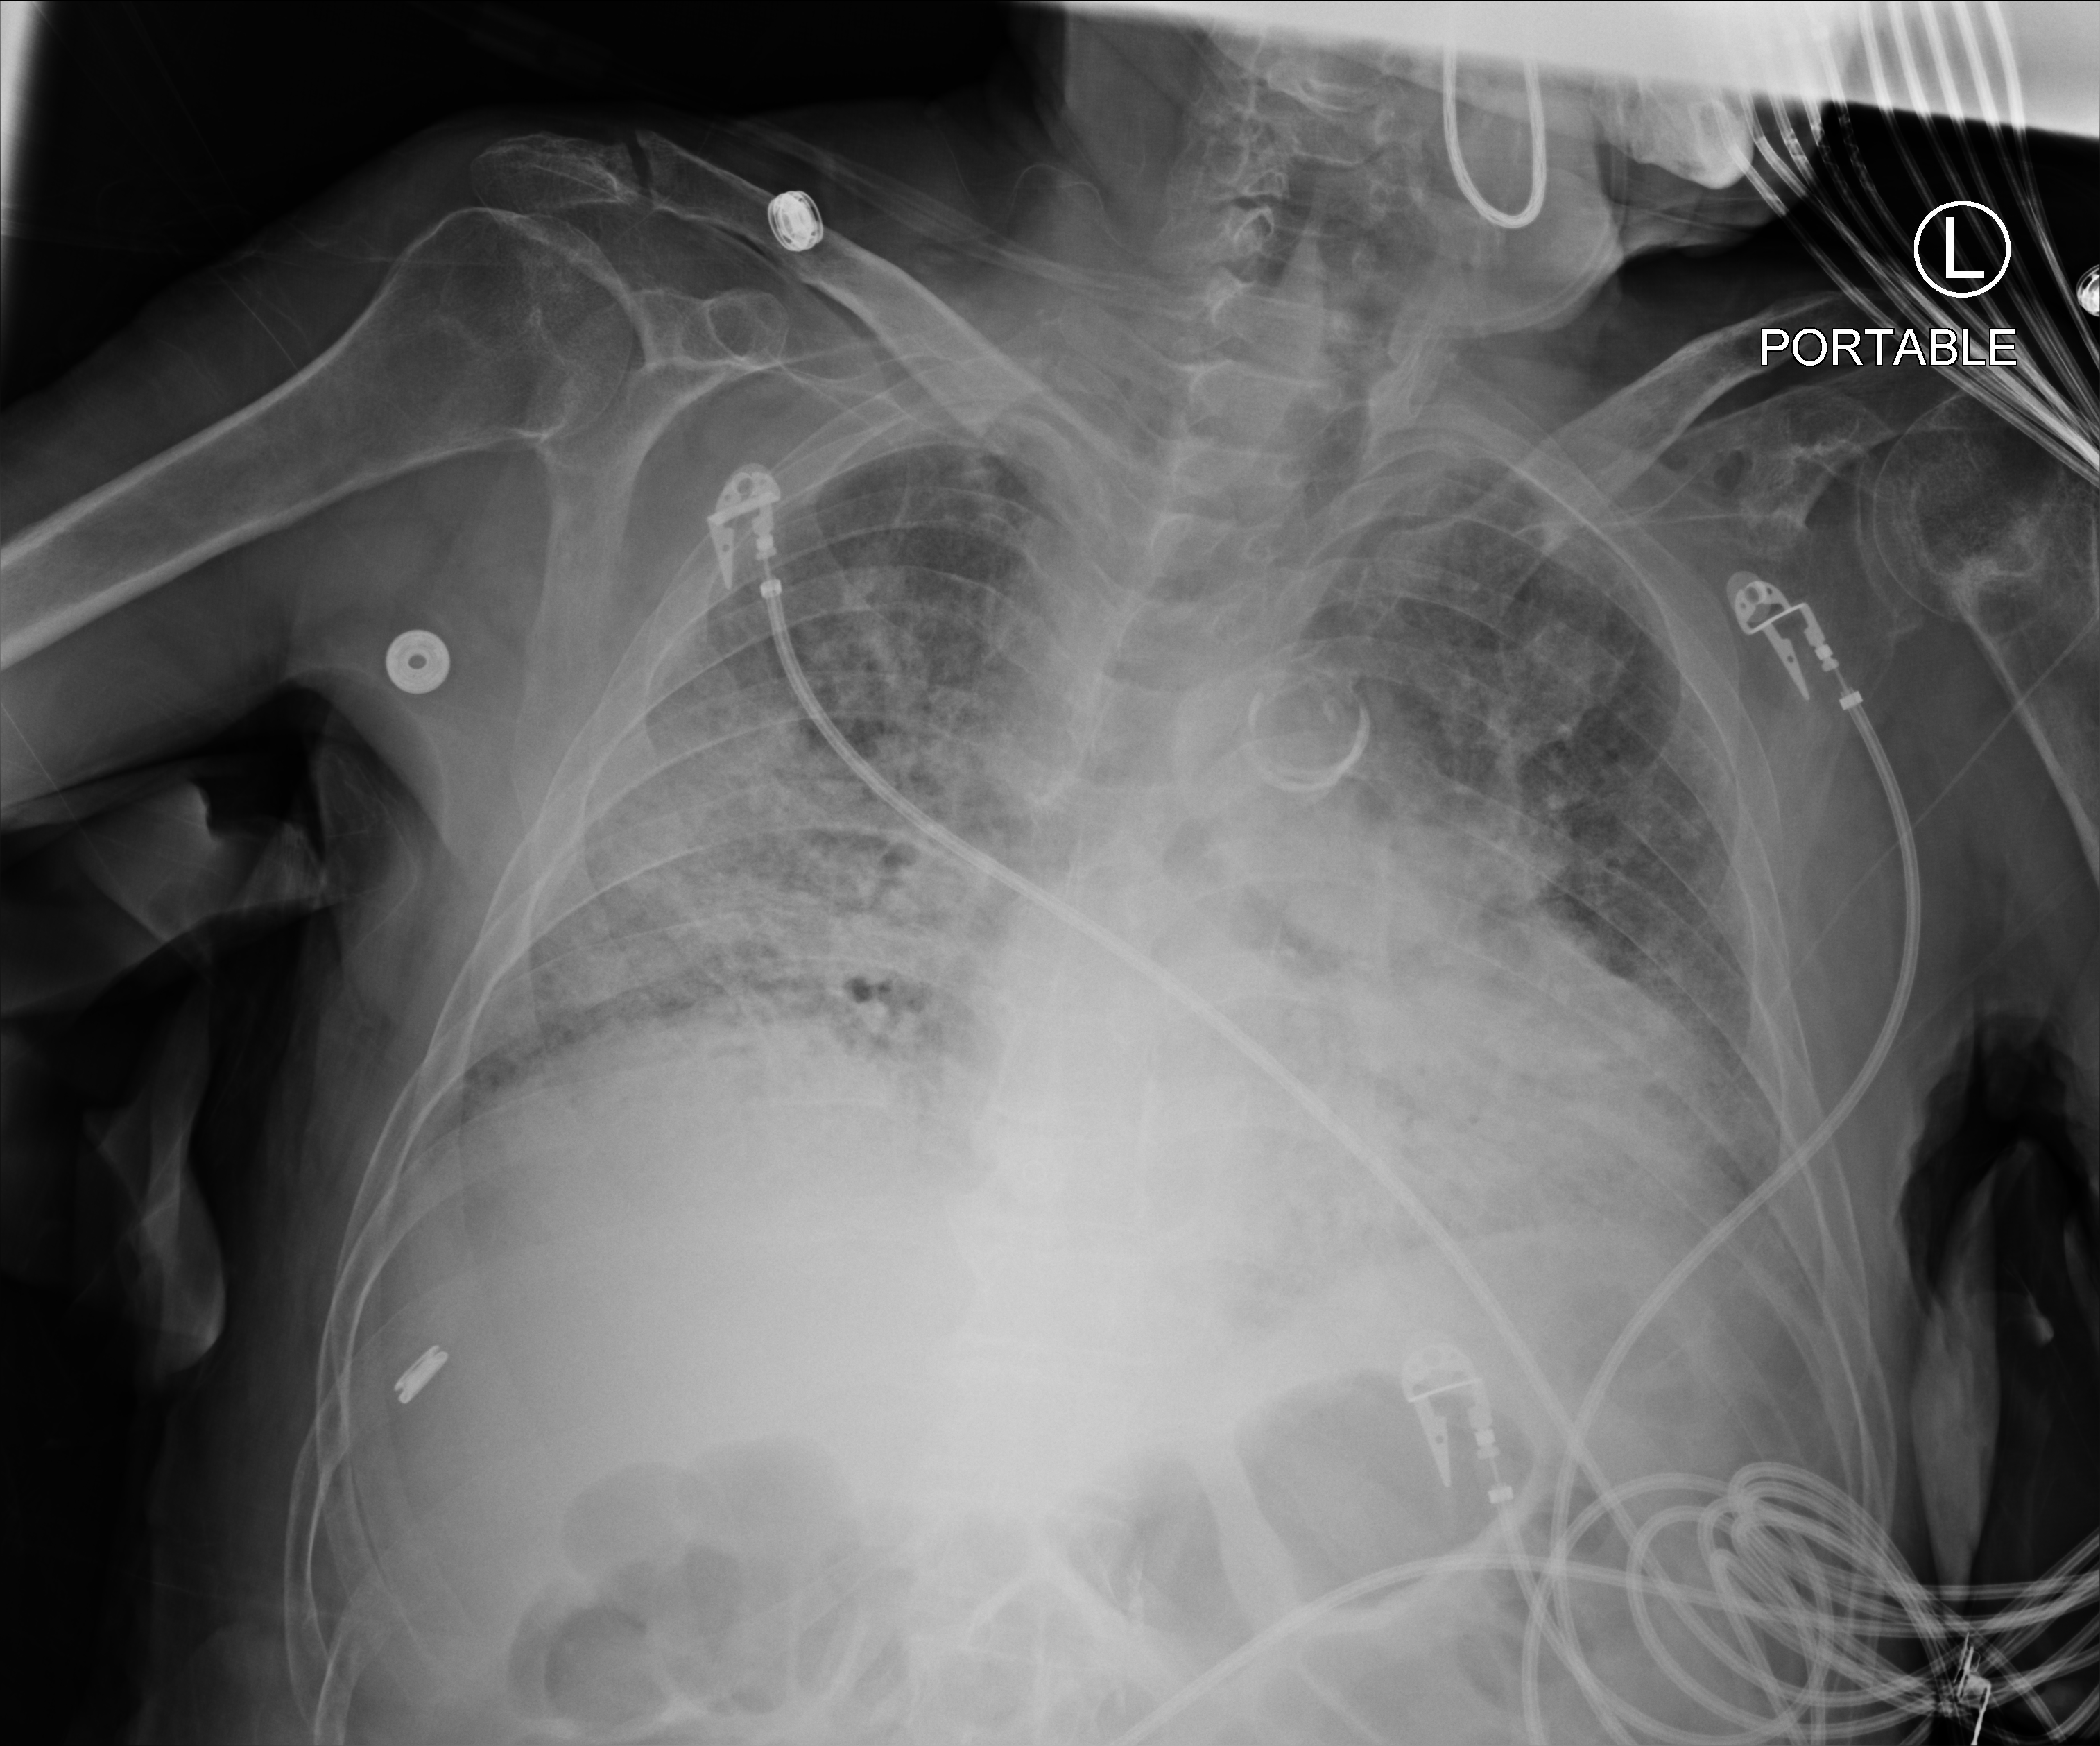
Chest X-ray (portable), anteroposterior (AP) projection. Male patient hospitalised with COVID-19, age 60–74 years.
From the hospital-stay record, not from the radiograph (when in the stay this image was taken is not recorded): COPD (admission record): no; smoking status (admission record): never.